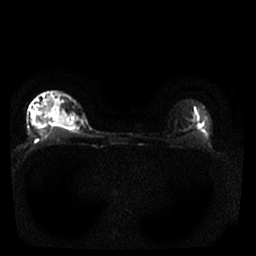
Breast MRI, one axial slice. Position 23 of 25 along the scan axis. Diffusion-weighted series; image 2 of 4 stored at this slice position (different b-values; order by instance number). 1.5 T. 4 mm slice thickness. 256 × 256 image matrix. Female patient.
Structures marked on this image (manually delineated by an expert):
- tumour on diffusion-weighted imaging: bounding box (x1, y1, x2, y2) in pixels: (56, 116, 66, 125)